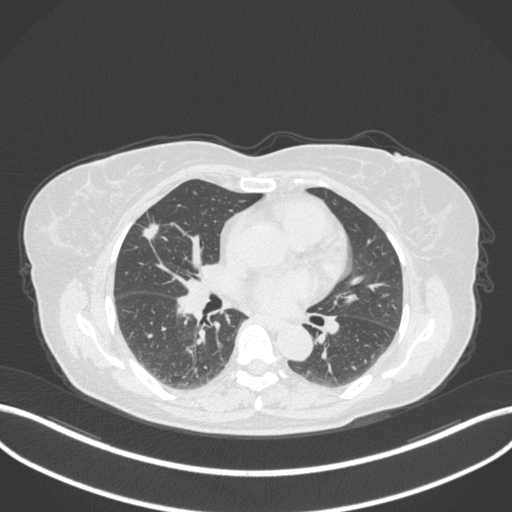
Chest CT, one axial slice; slice 174 of 310 in the series (ordered by position); reconstruction kernel B31f; 120 kVp; lung window (W 1500 / L -600 HU); 512 × 512 image matrix, field of view 400 × 400 mm. Patient: female, 55 years. Case-level facts recorded for this patient, not image findings: clinical TNM (as recorded): T1b N0 M0.
Outlined on this slice (bounding box drawn by a radiologist):
- lung tumour (recorded histology: adenocarcinoma): bounding box <139,218,163,243> (left, top, right, bottom; pixels)